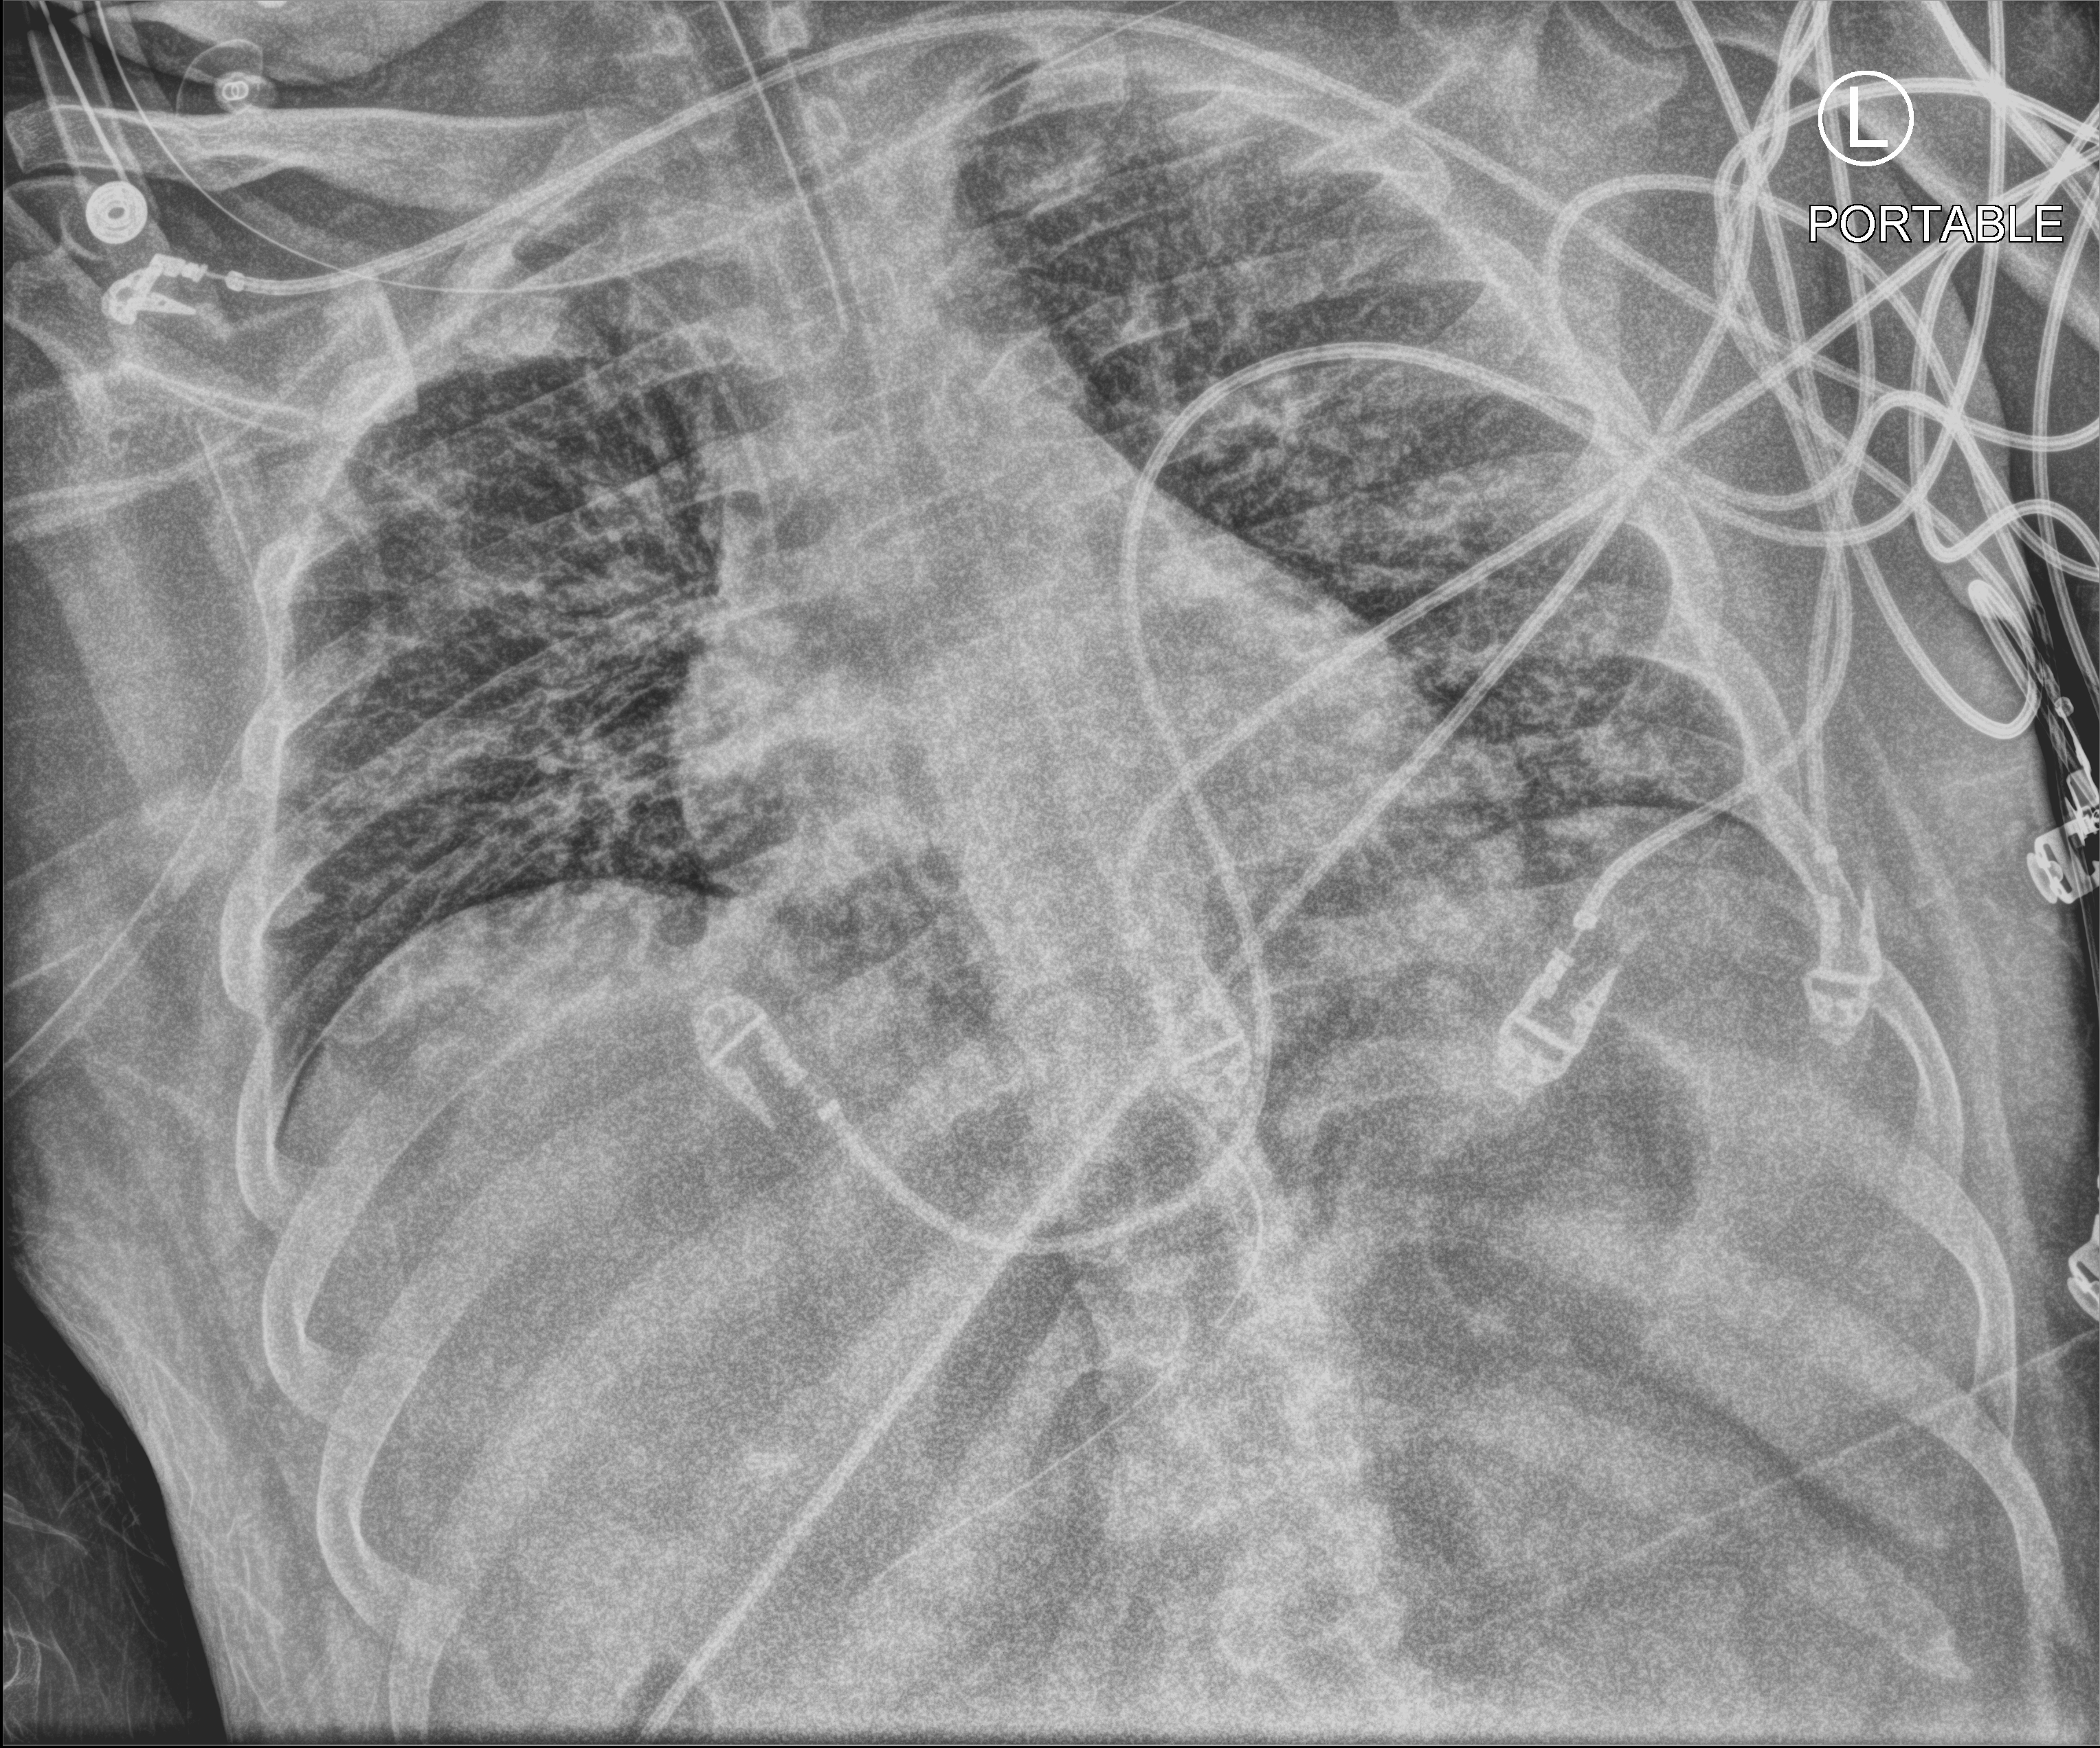
Portable chest radiograph, anteroposterior (AP) projection. Male patient hospitalised with COVID-19, age 18–59 years.
From the hospital-stay record, not from the radiograph (when in the stay this image was taken is not recorded):
- admitted to intensive care during this hospital stay: yes
- mechanically ventilated during this hospital stay: yes